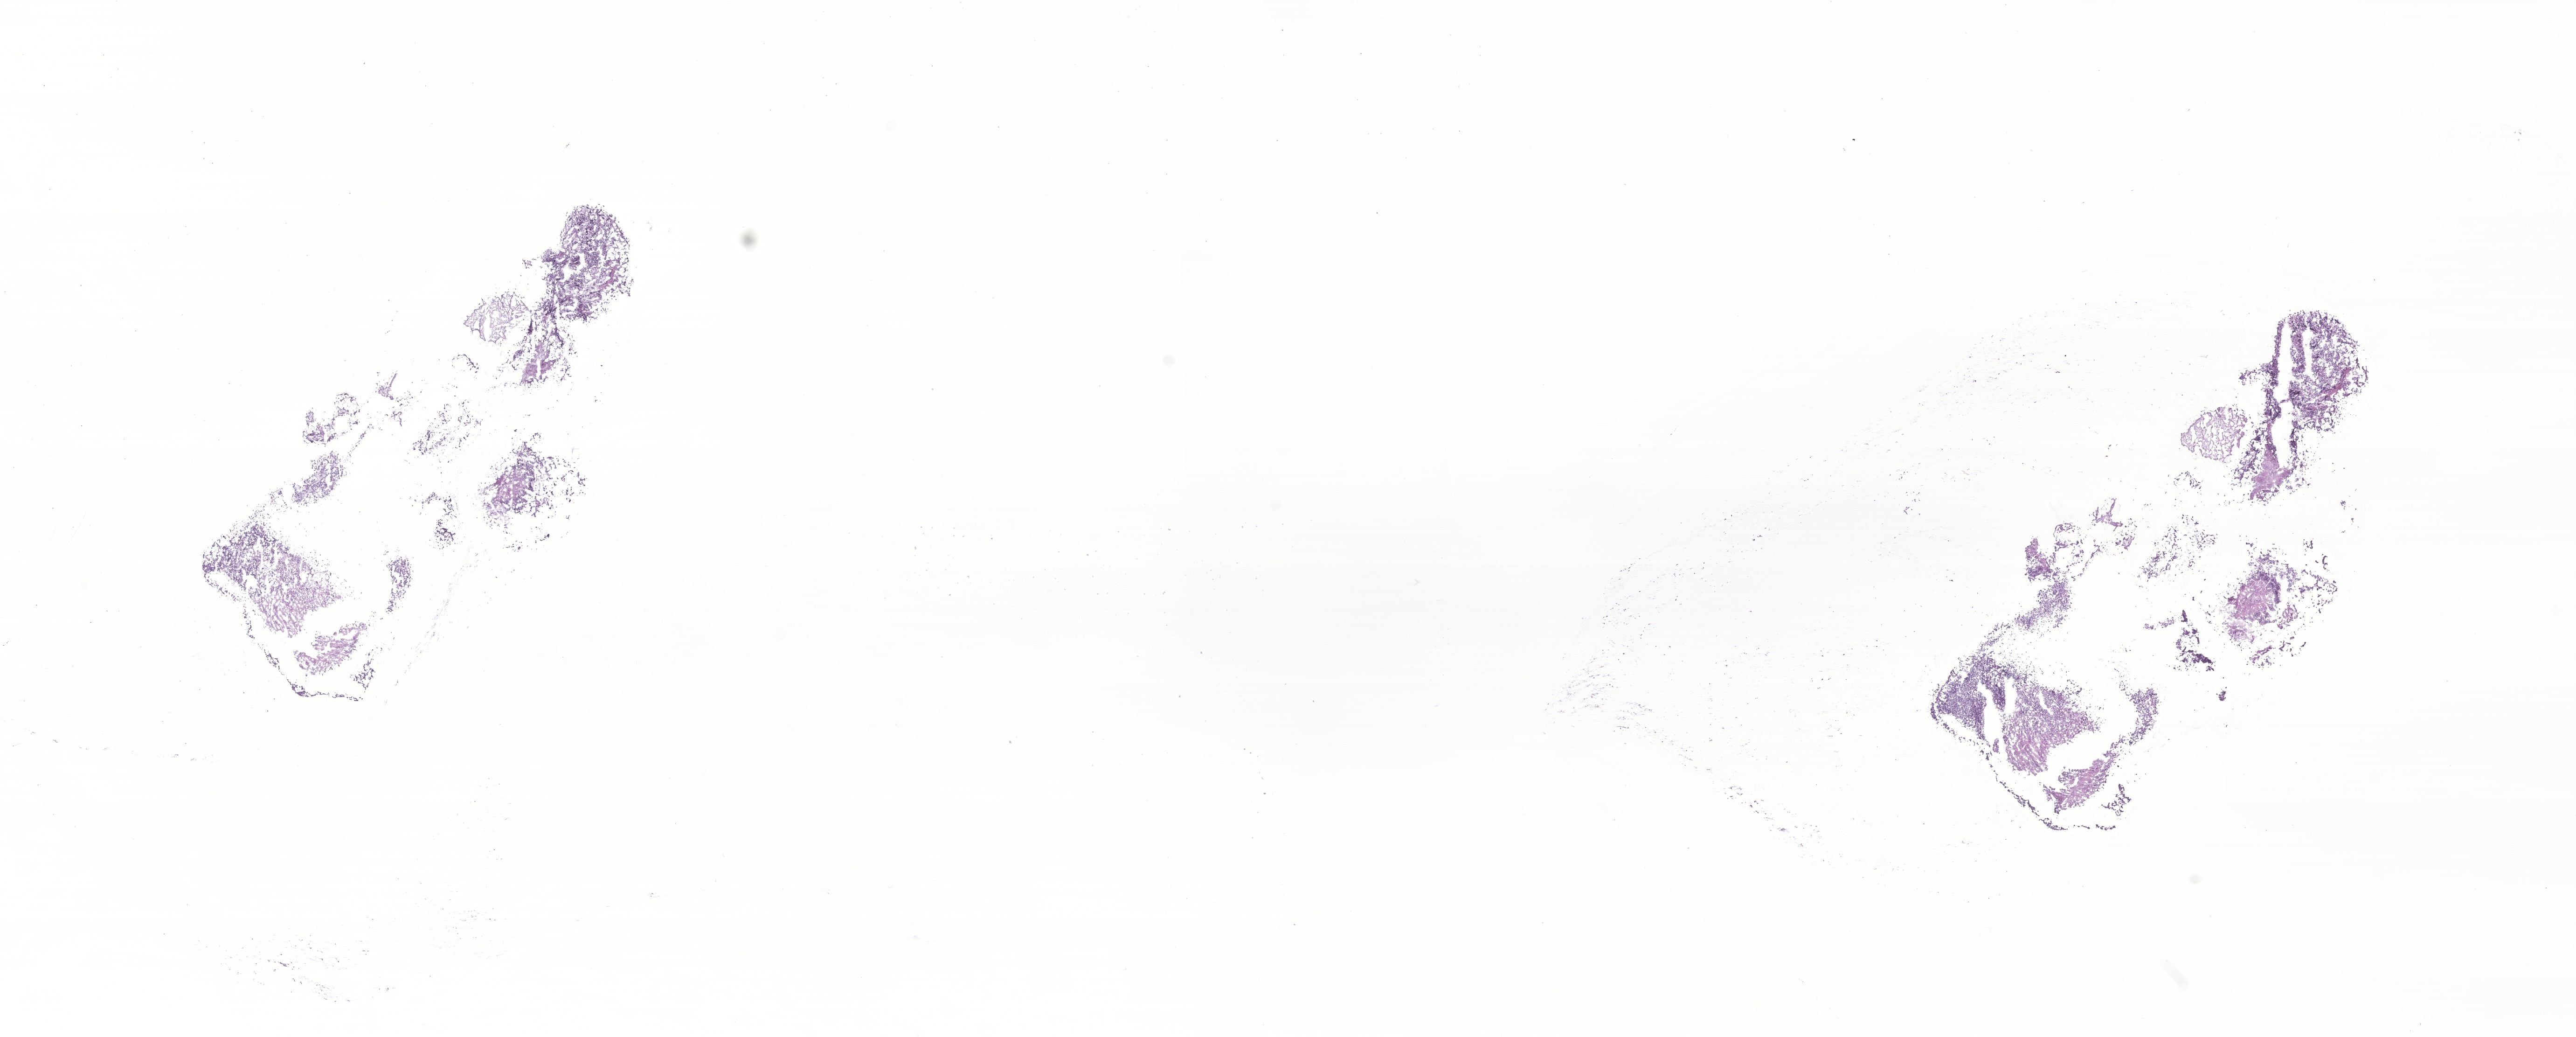
Digitized H&E-stained section of tumor tissue from the brain, whole scanned area (about 23.3 x 9.4 mm) shown as a low-resolution overview. Cryosection (OCT / tissue freezing medium). Patient female; age 65 months (5 years 5 months).
Recorded diagnosis: Medulloblastoma, NOS.